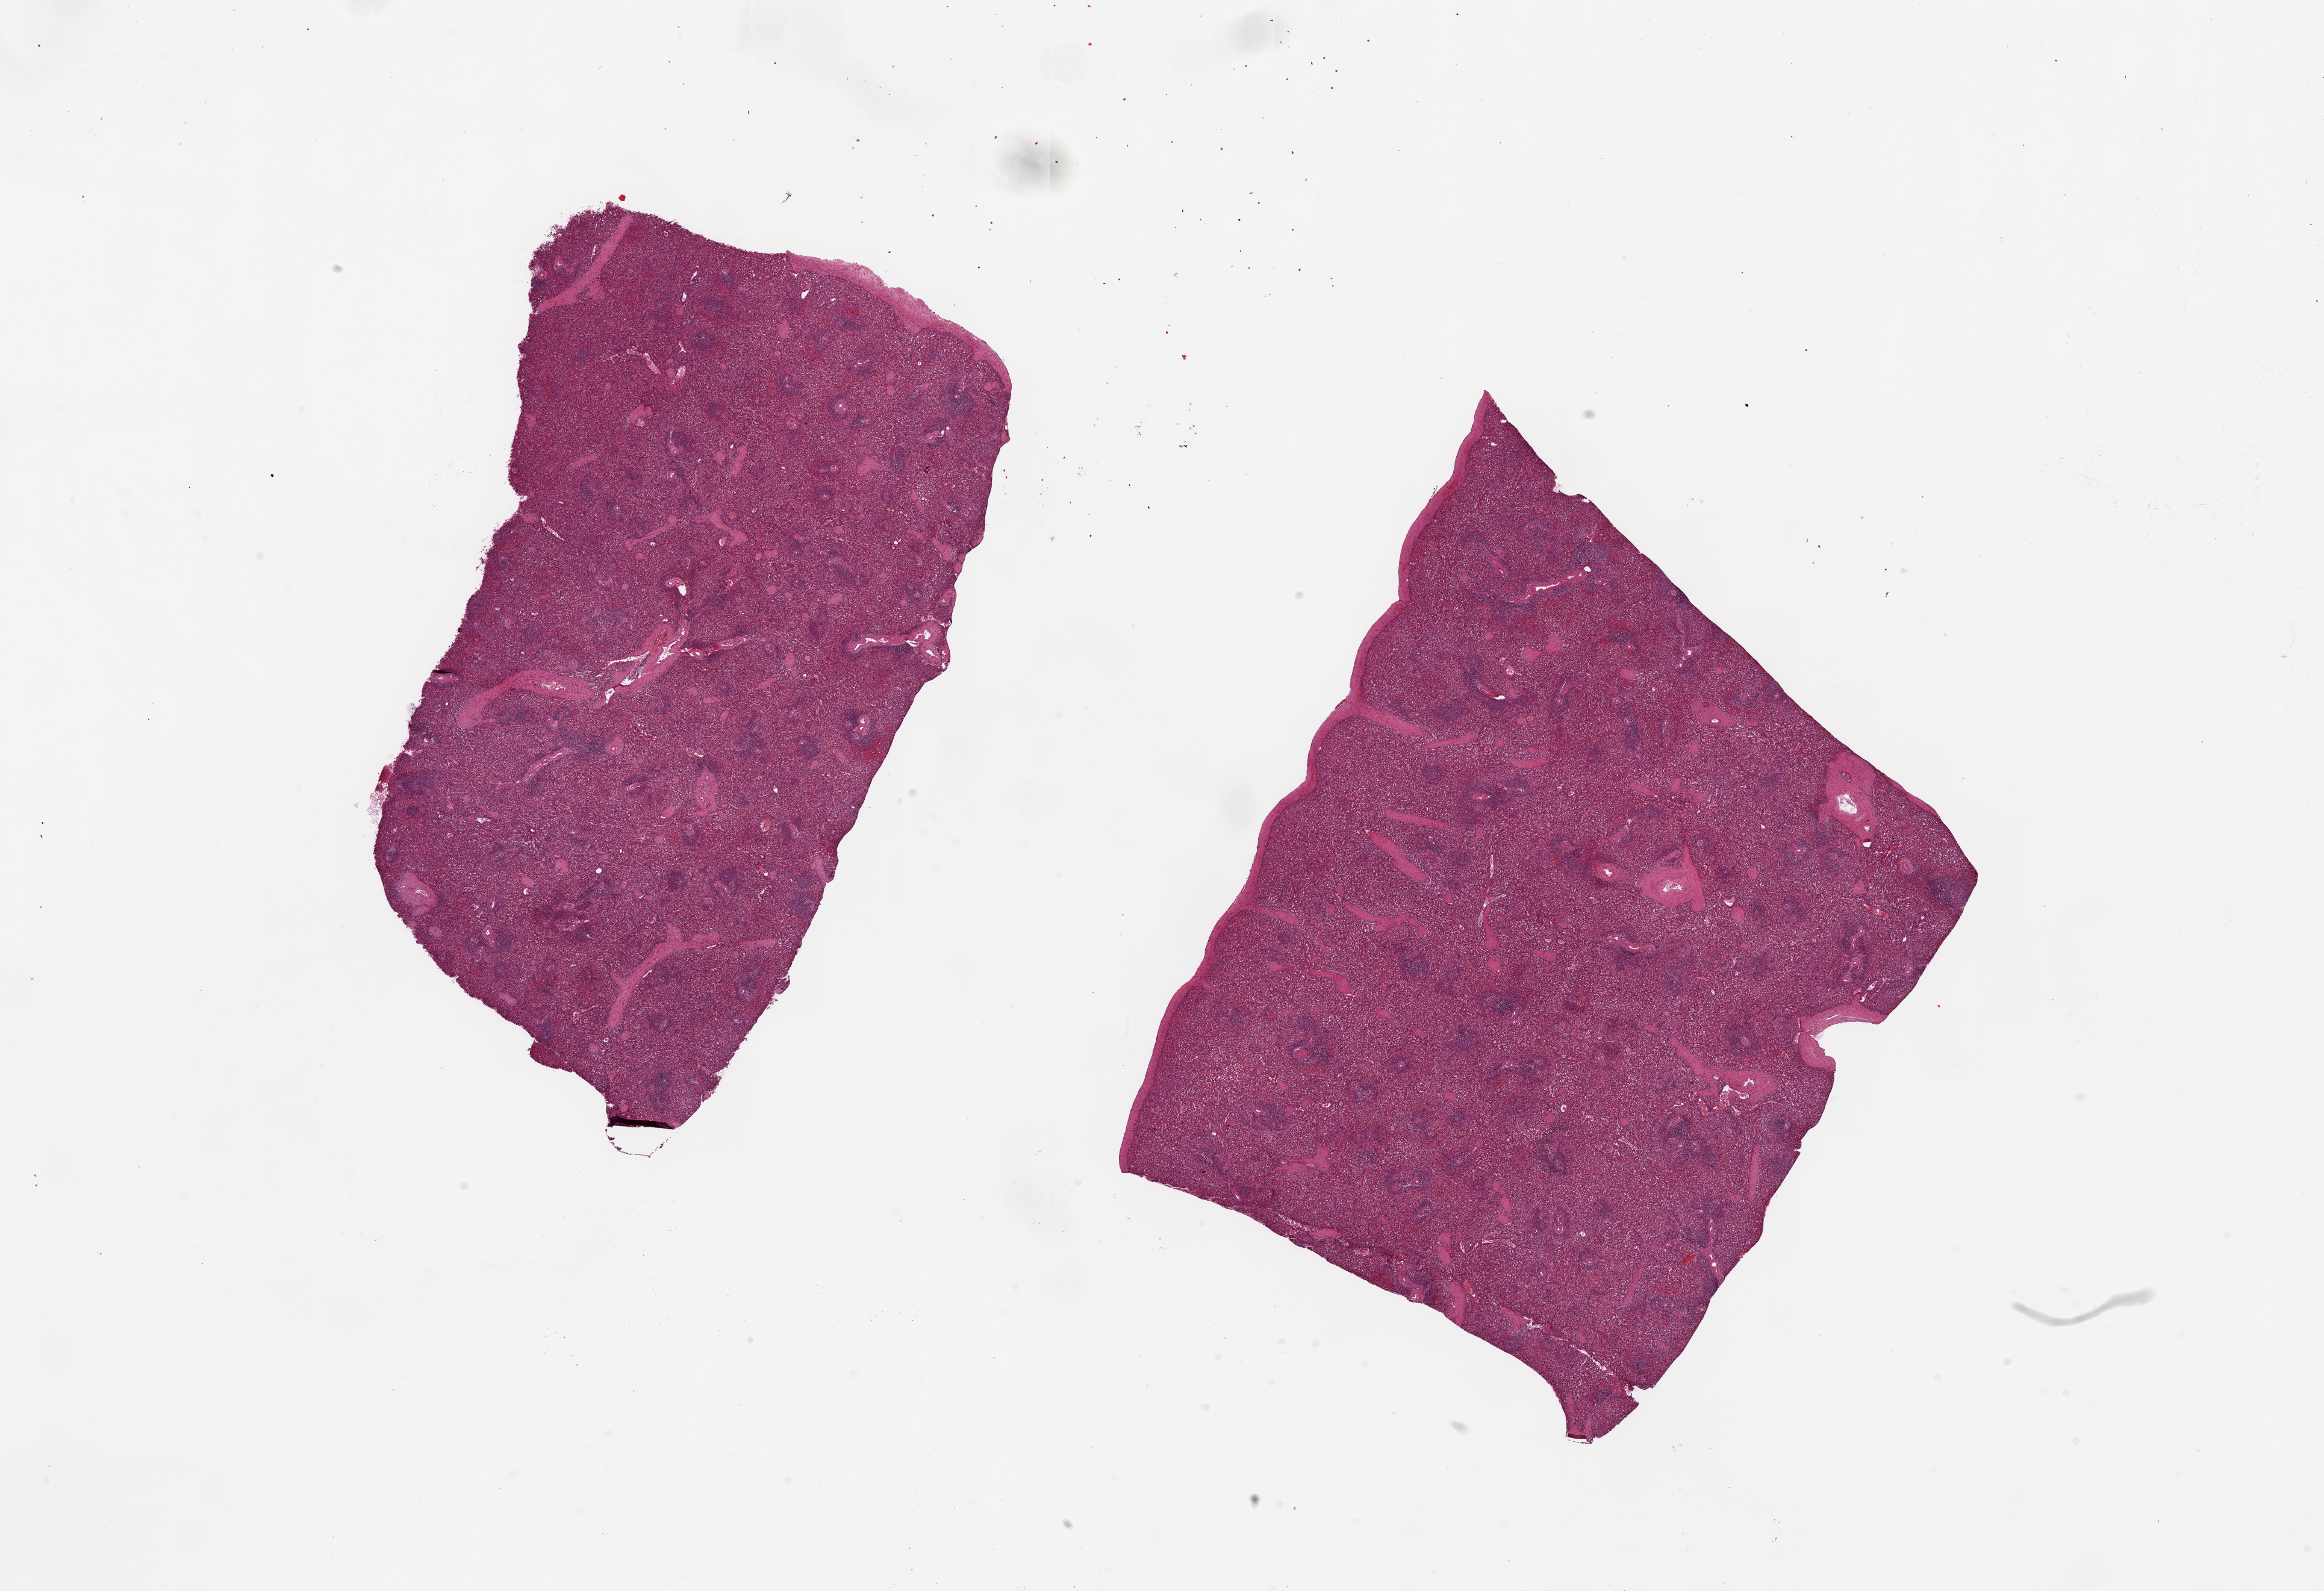
Whole-slide image, haematoxylin and eosin stain, brightfield, low-resolution overview of the scanned area, about 30.5 x 20.9 mm. PAXgene-fixed paraffin-embedded (PFPE) section. Sampled site (target tissue): spleen. Tissue donor sample. Female donor.
Reviewer comment on this tissue sample: 2 pieces, 12x7 & 12x9mm; moderate congestion.